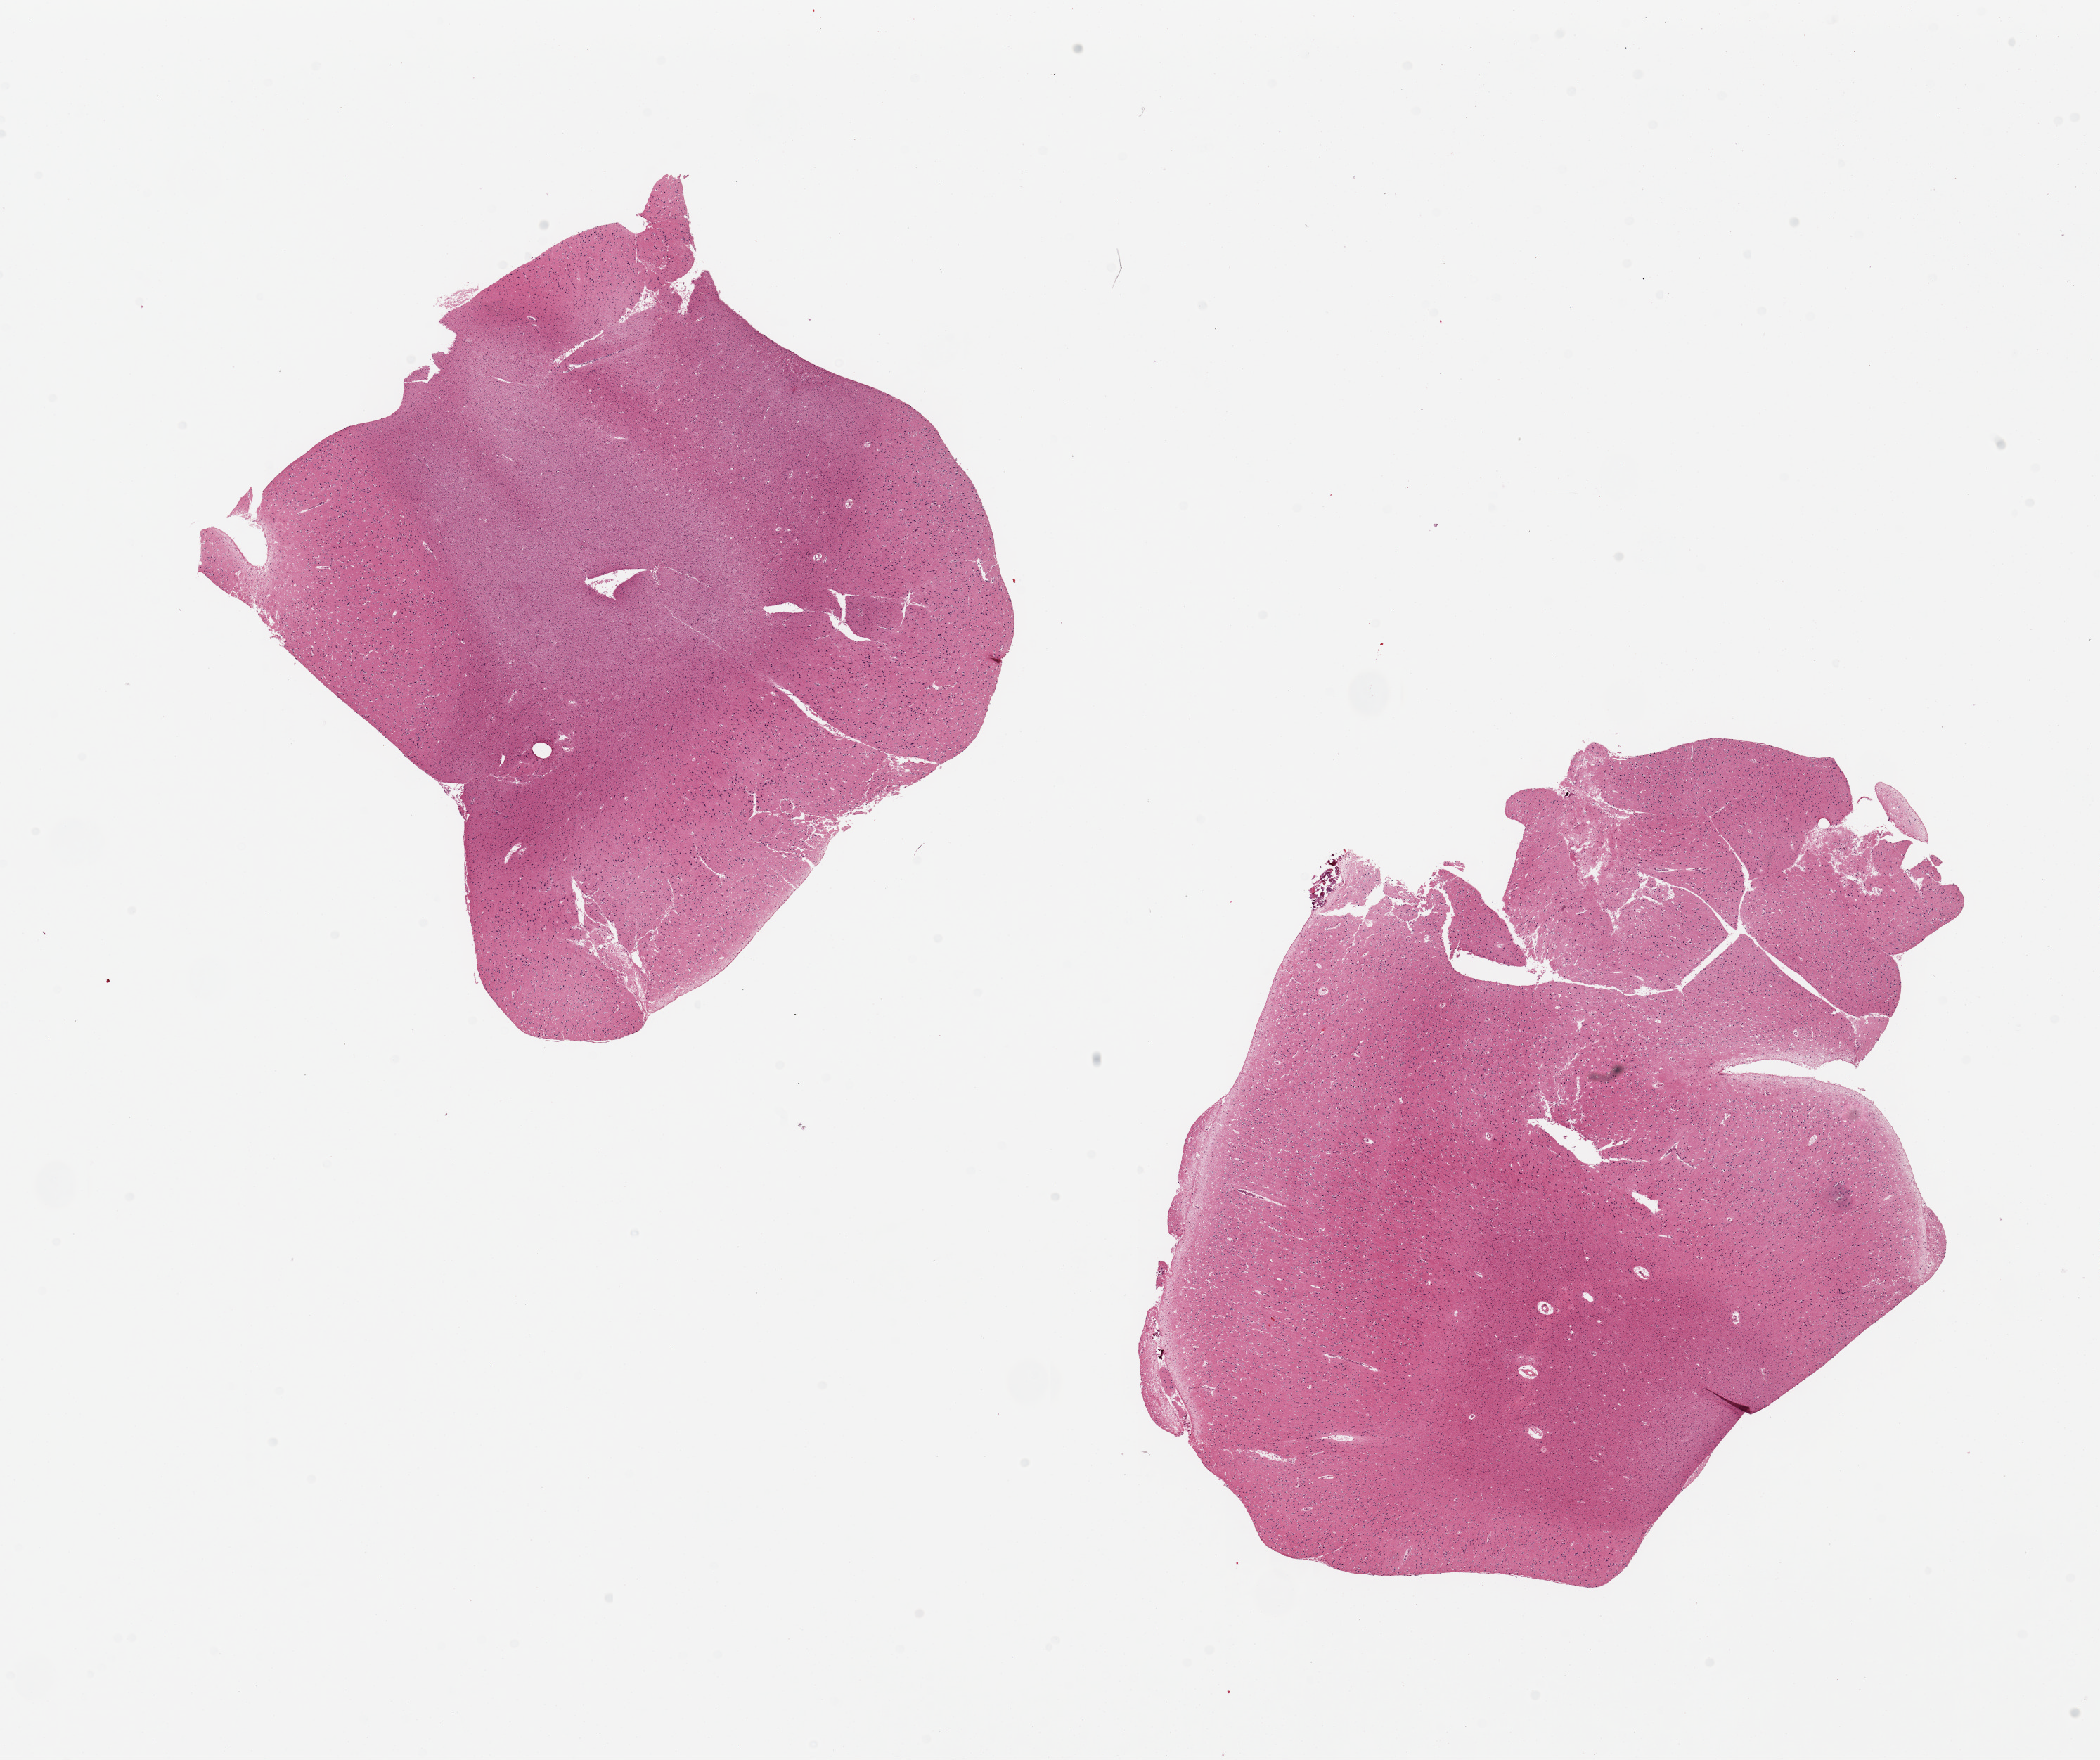
Digitized hematoxylin and eosin (H&E)-stained section — shown as a low-resolution overview of the whole scanned area (about 23.6 x 19.8 mm); PAXgene-fixed, paraffin-embedded tissue; sampled site (target tissue): cerebral cortex; donor tissue sample. Male donor.
Pathologist's review note for this sample: 2 pieces.